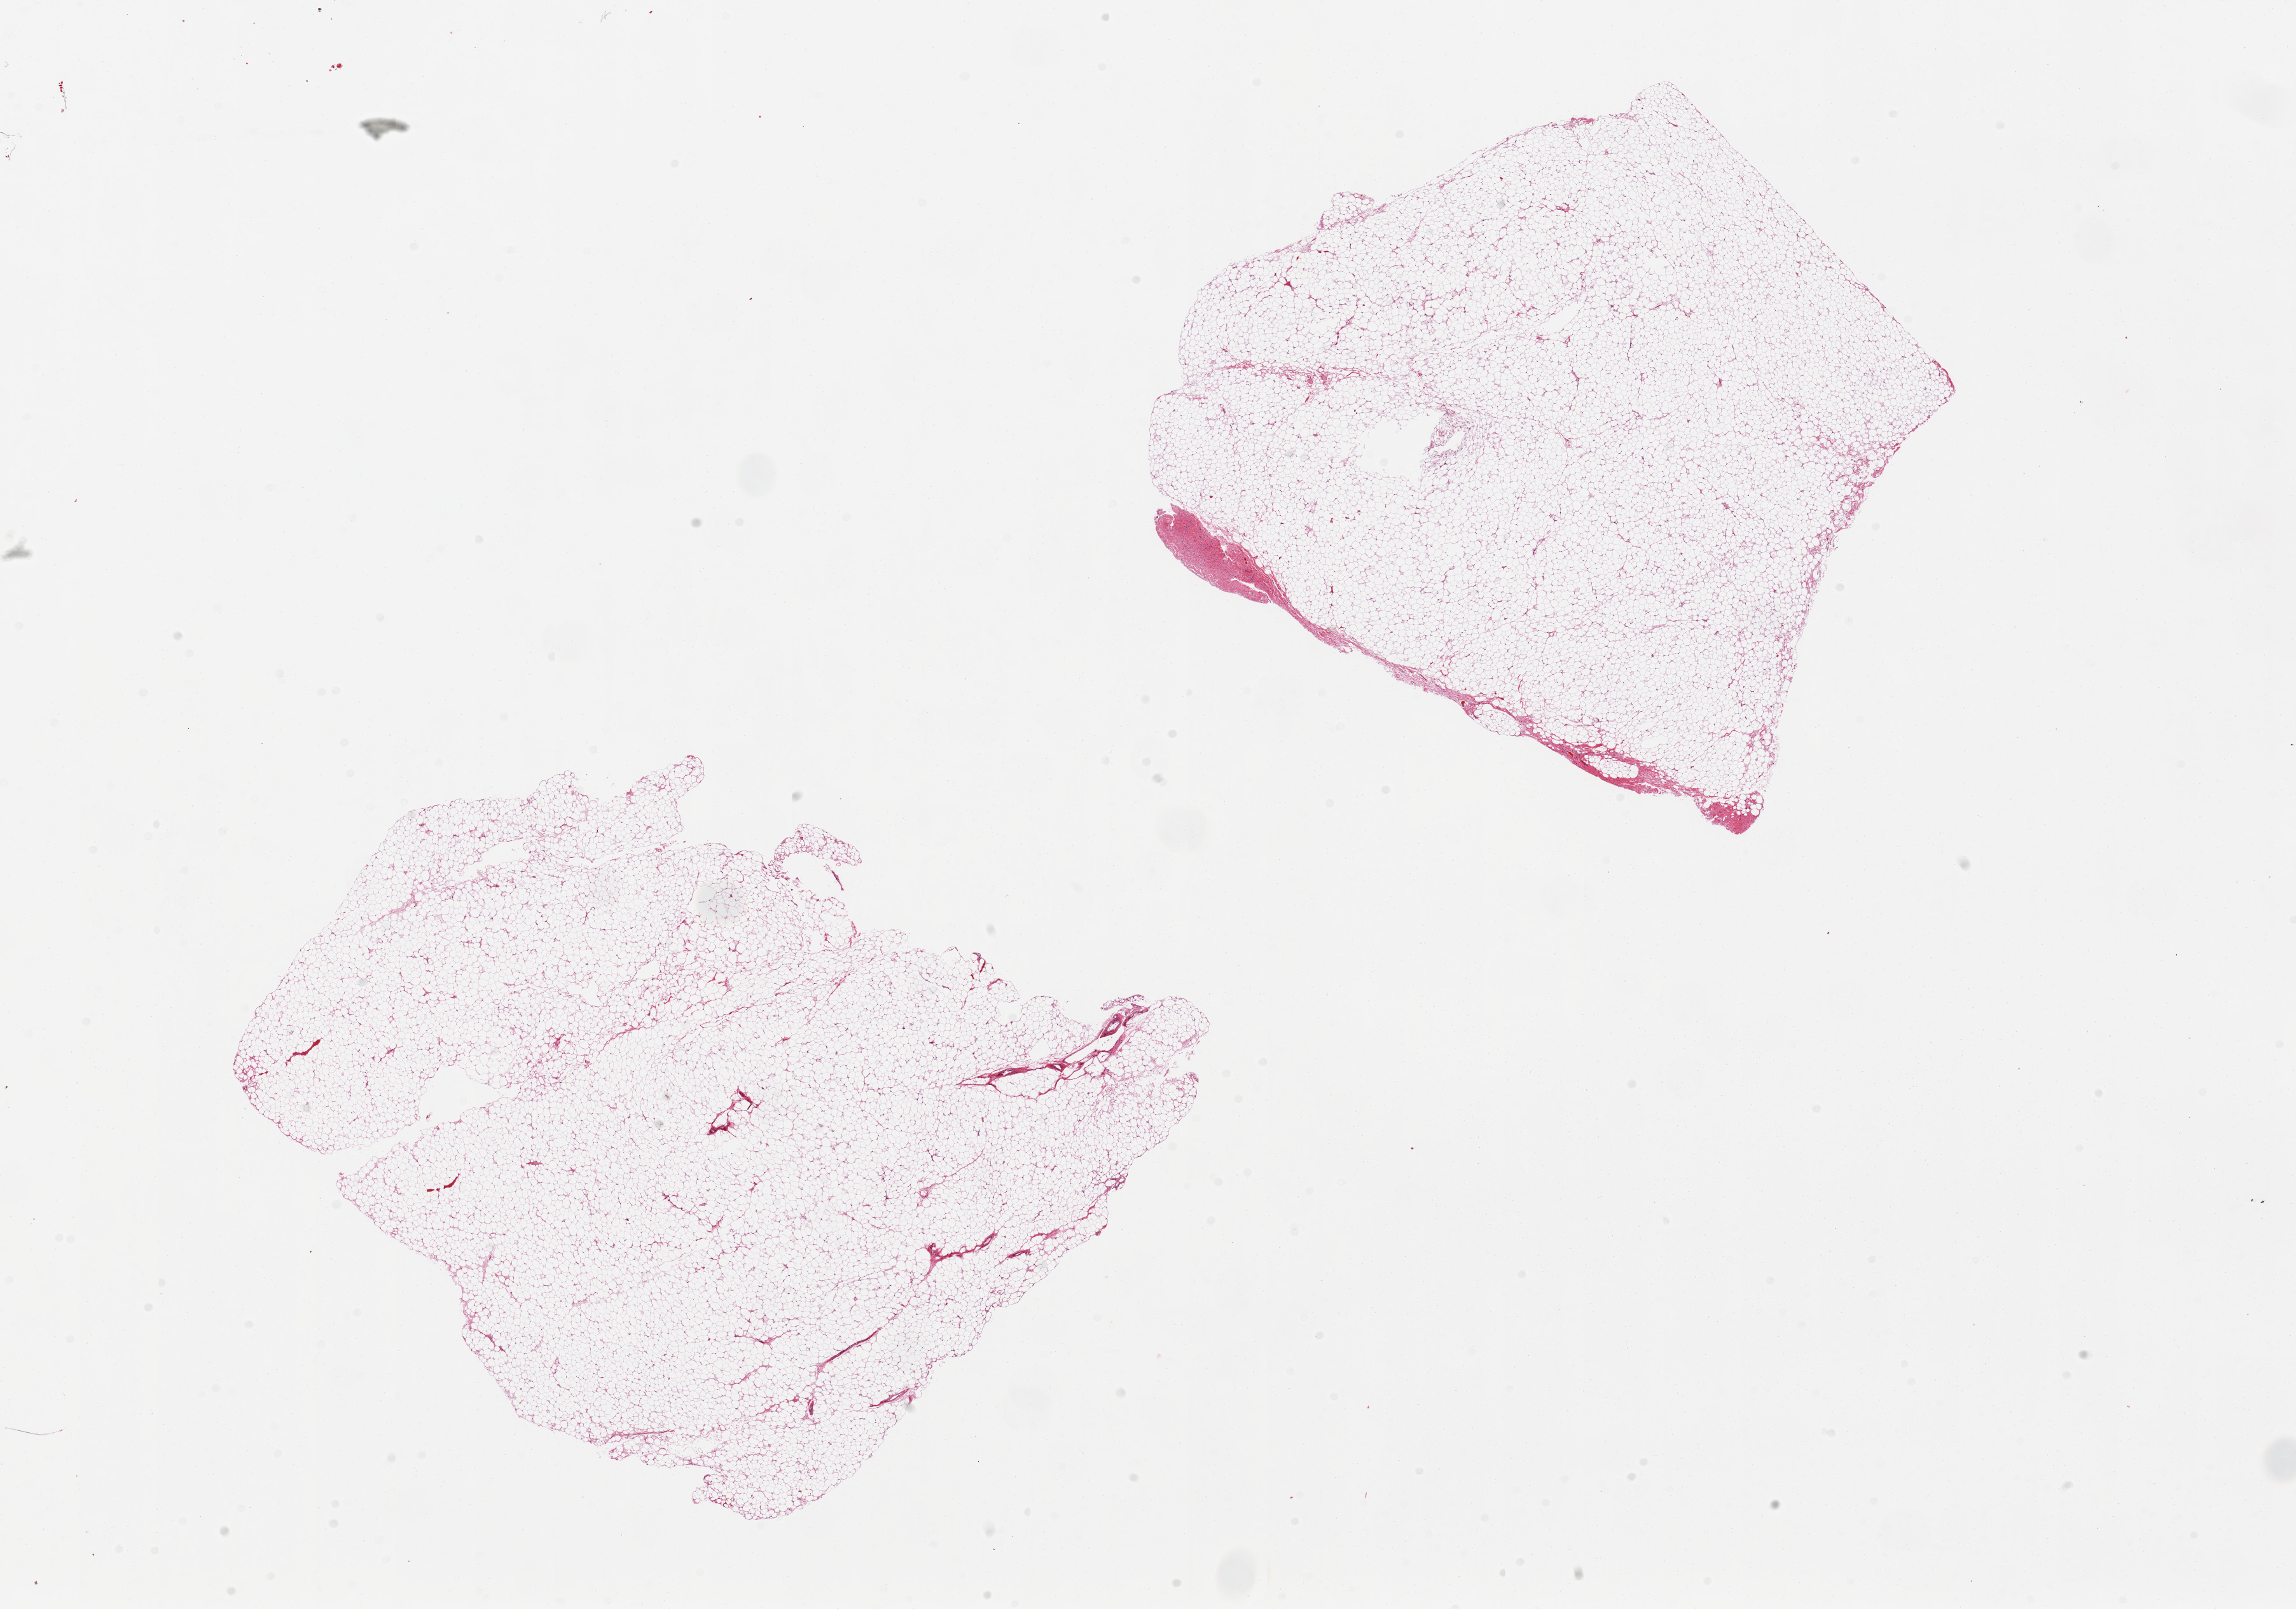
Hematoxylin and eosin (H&E) whole-slide image — low-resolution overview of the scanned area, about 28.5 x 20.0 mm (from a 20x scan); PAXgene-fixed paraffin-embedded (PFPE) section; section of adrenal gland (target tissue); donor tissue sample. Donor sex: male.
Reviewer comment on this tissue sample: 2 pieces, all adipose tissue, unknown provenance.